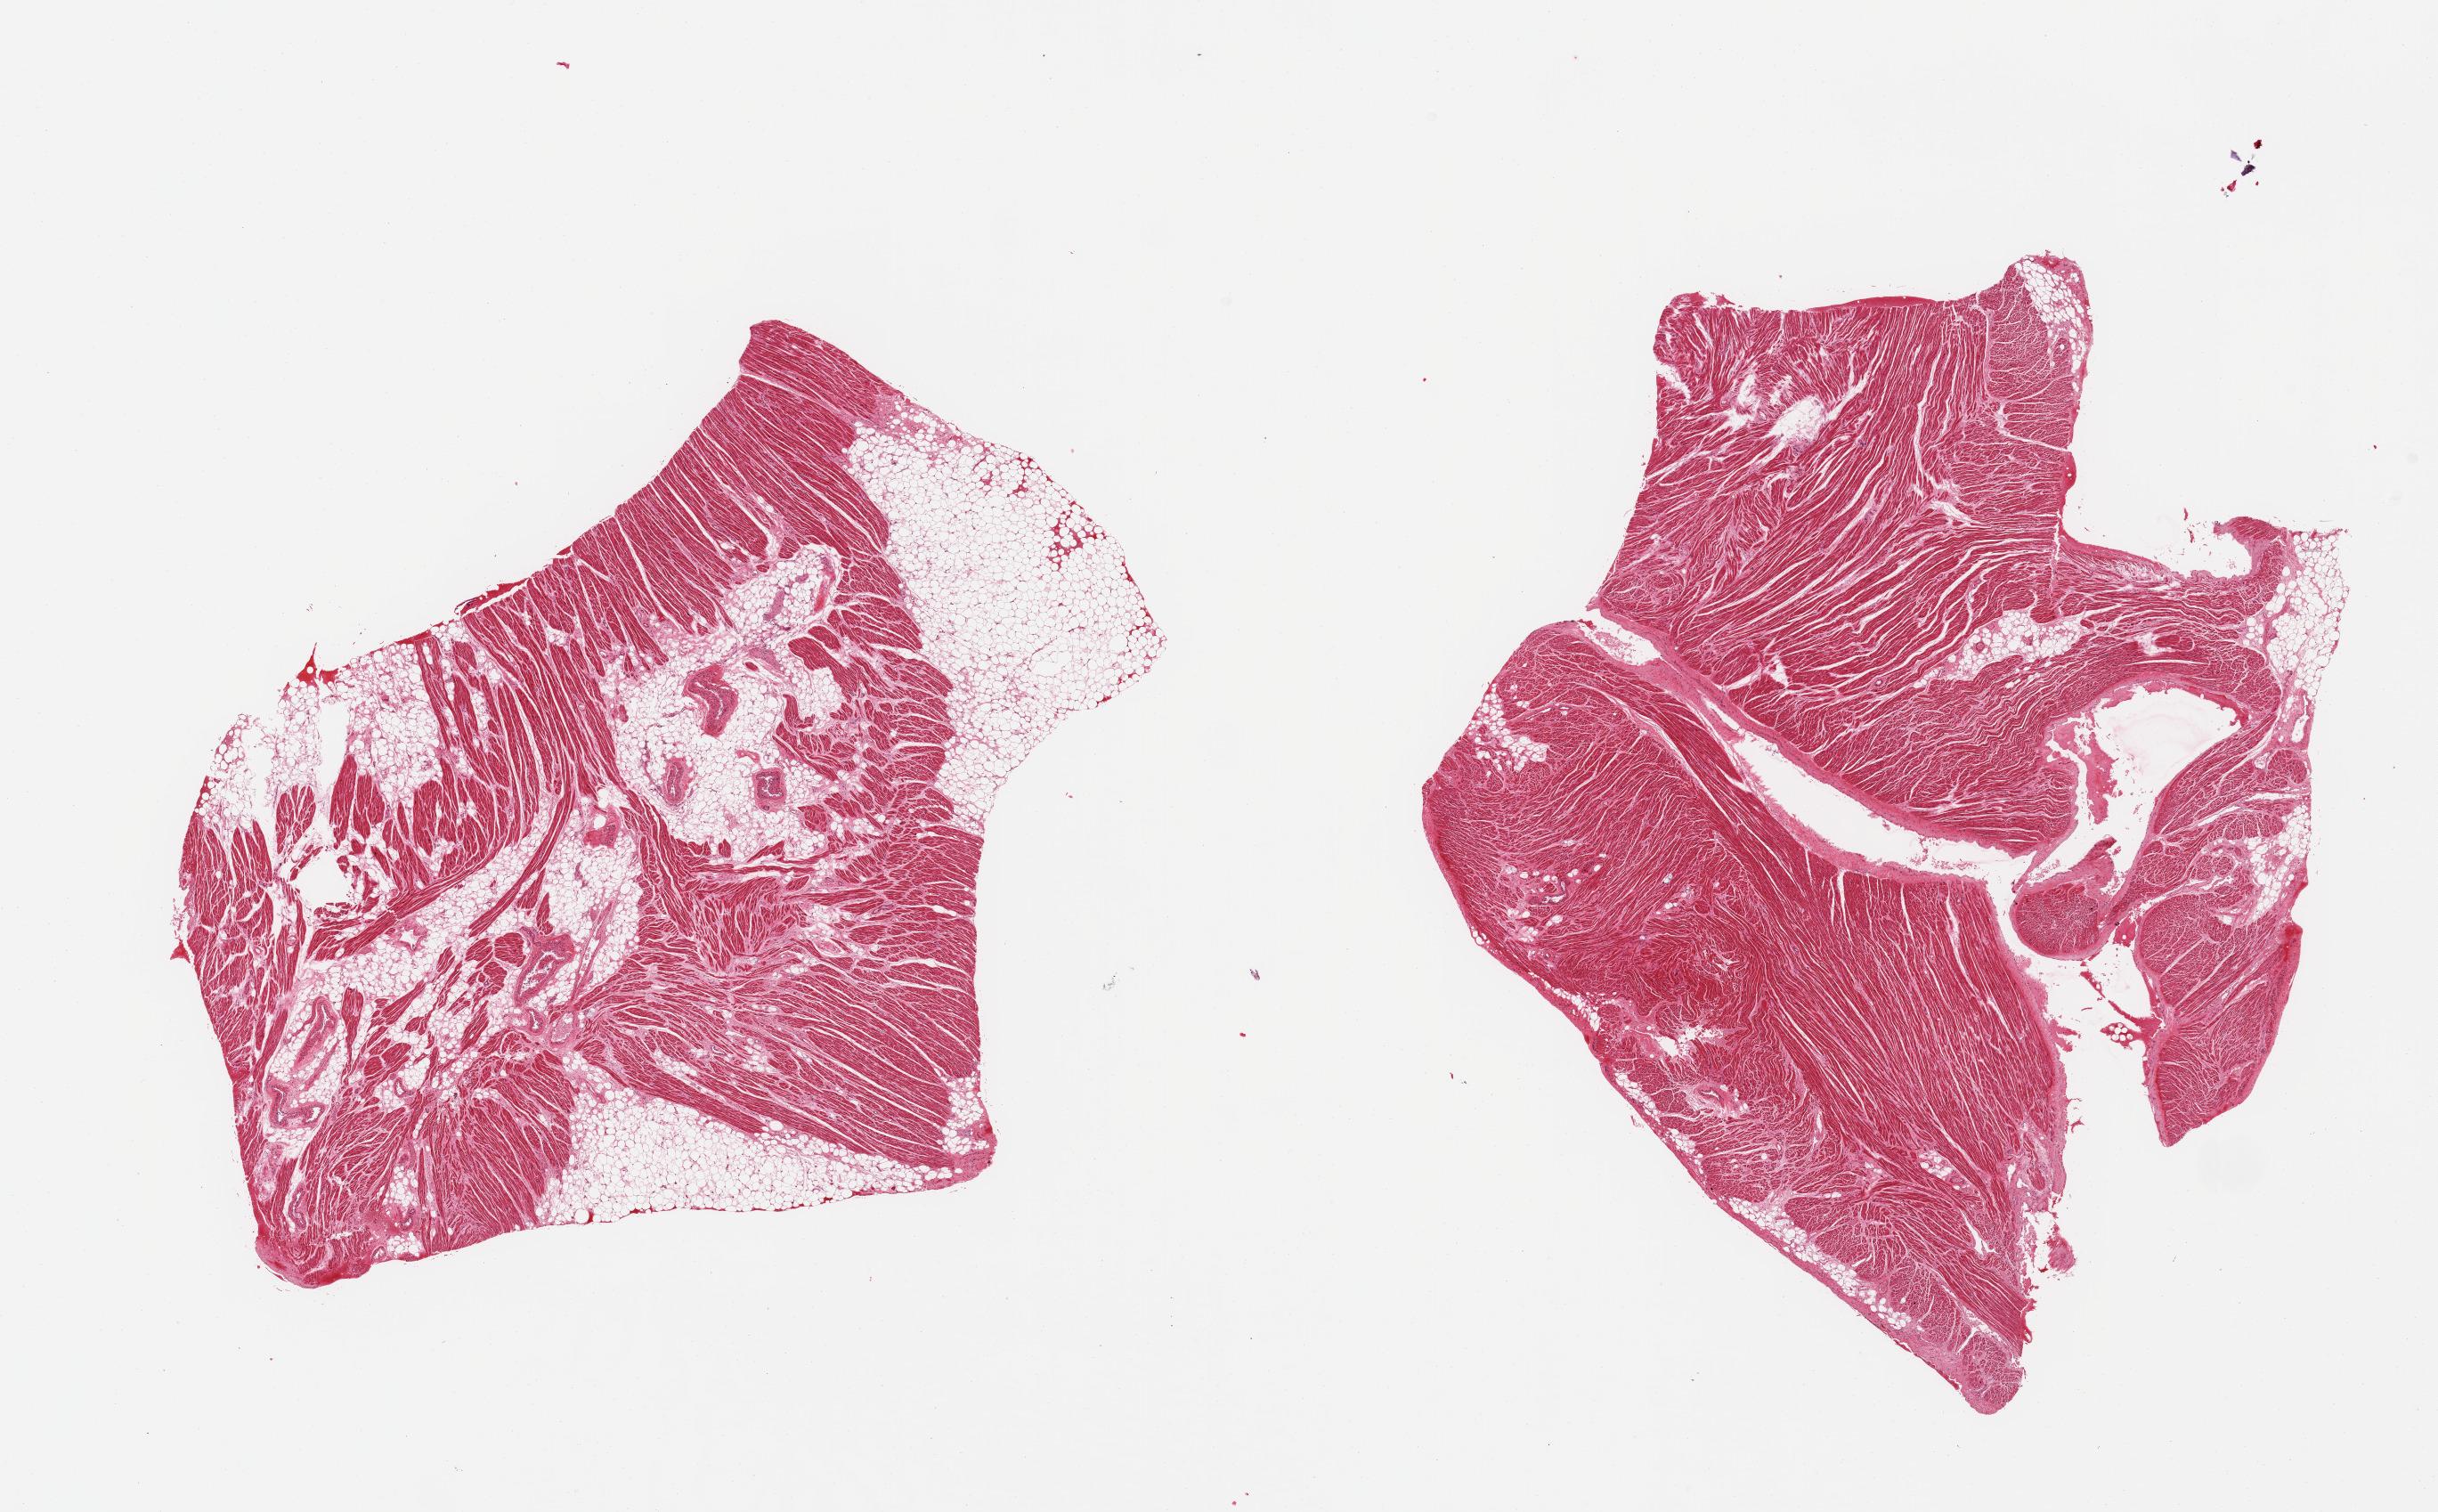
Hematoxylin and eosin (H&E) whole-slide image — low-resolution overview of the scanned area, about 21.7 x 13.4 mm (acquisition: 20x scan); PAXgene-fixed paraffin-embedded (PFPE) section; sampled site (target tissue): auricular appendage; donor tissue sample.
Reviewer comment on this tissue sample: 2 pieces, no abnormalities.